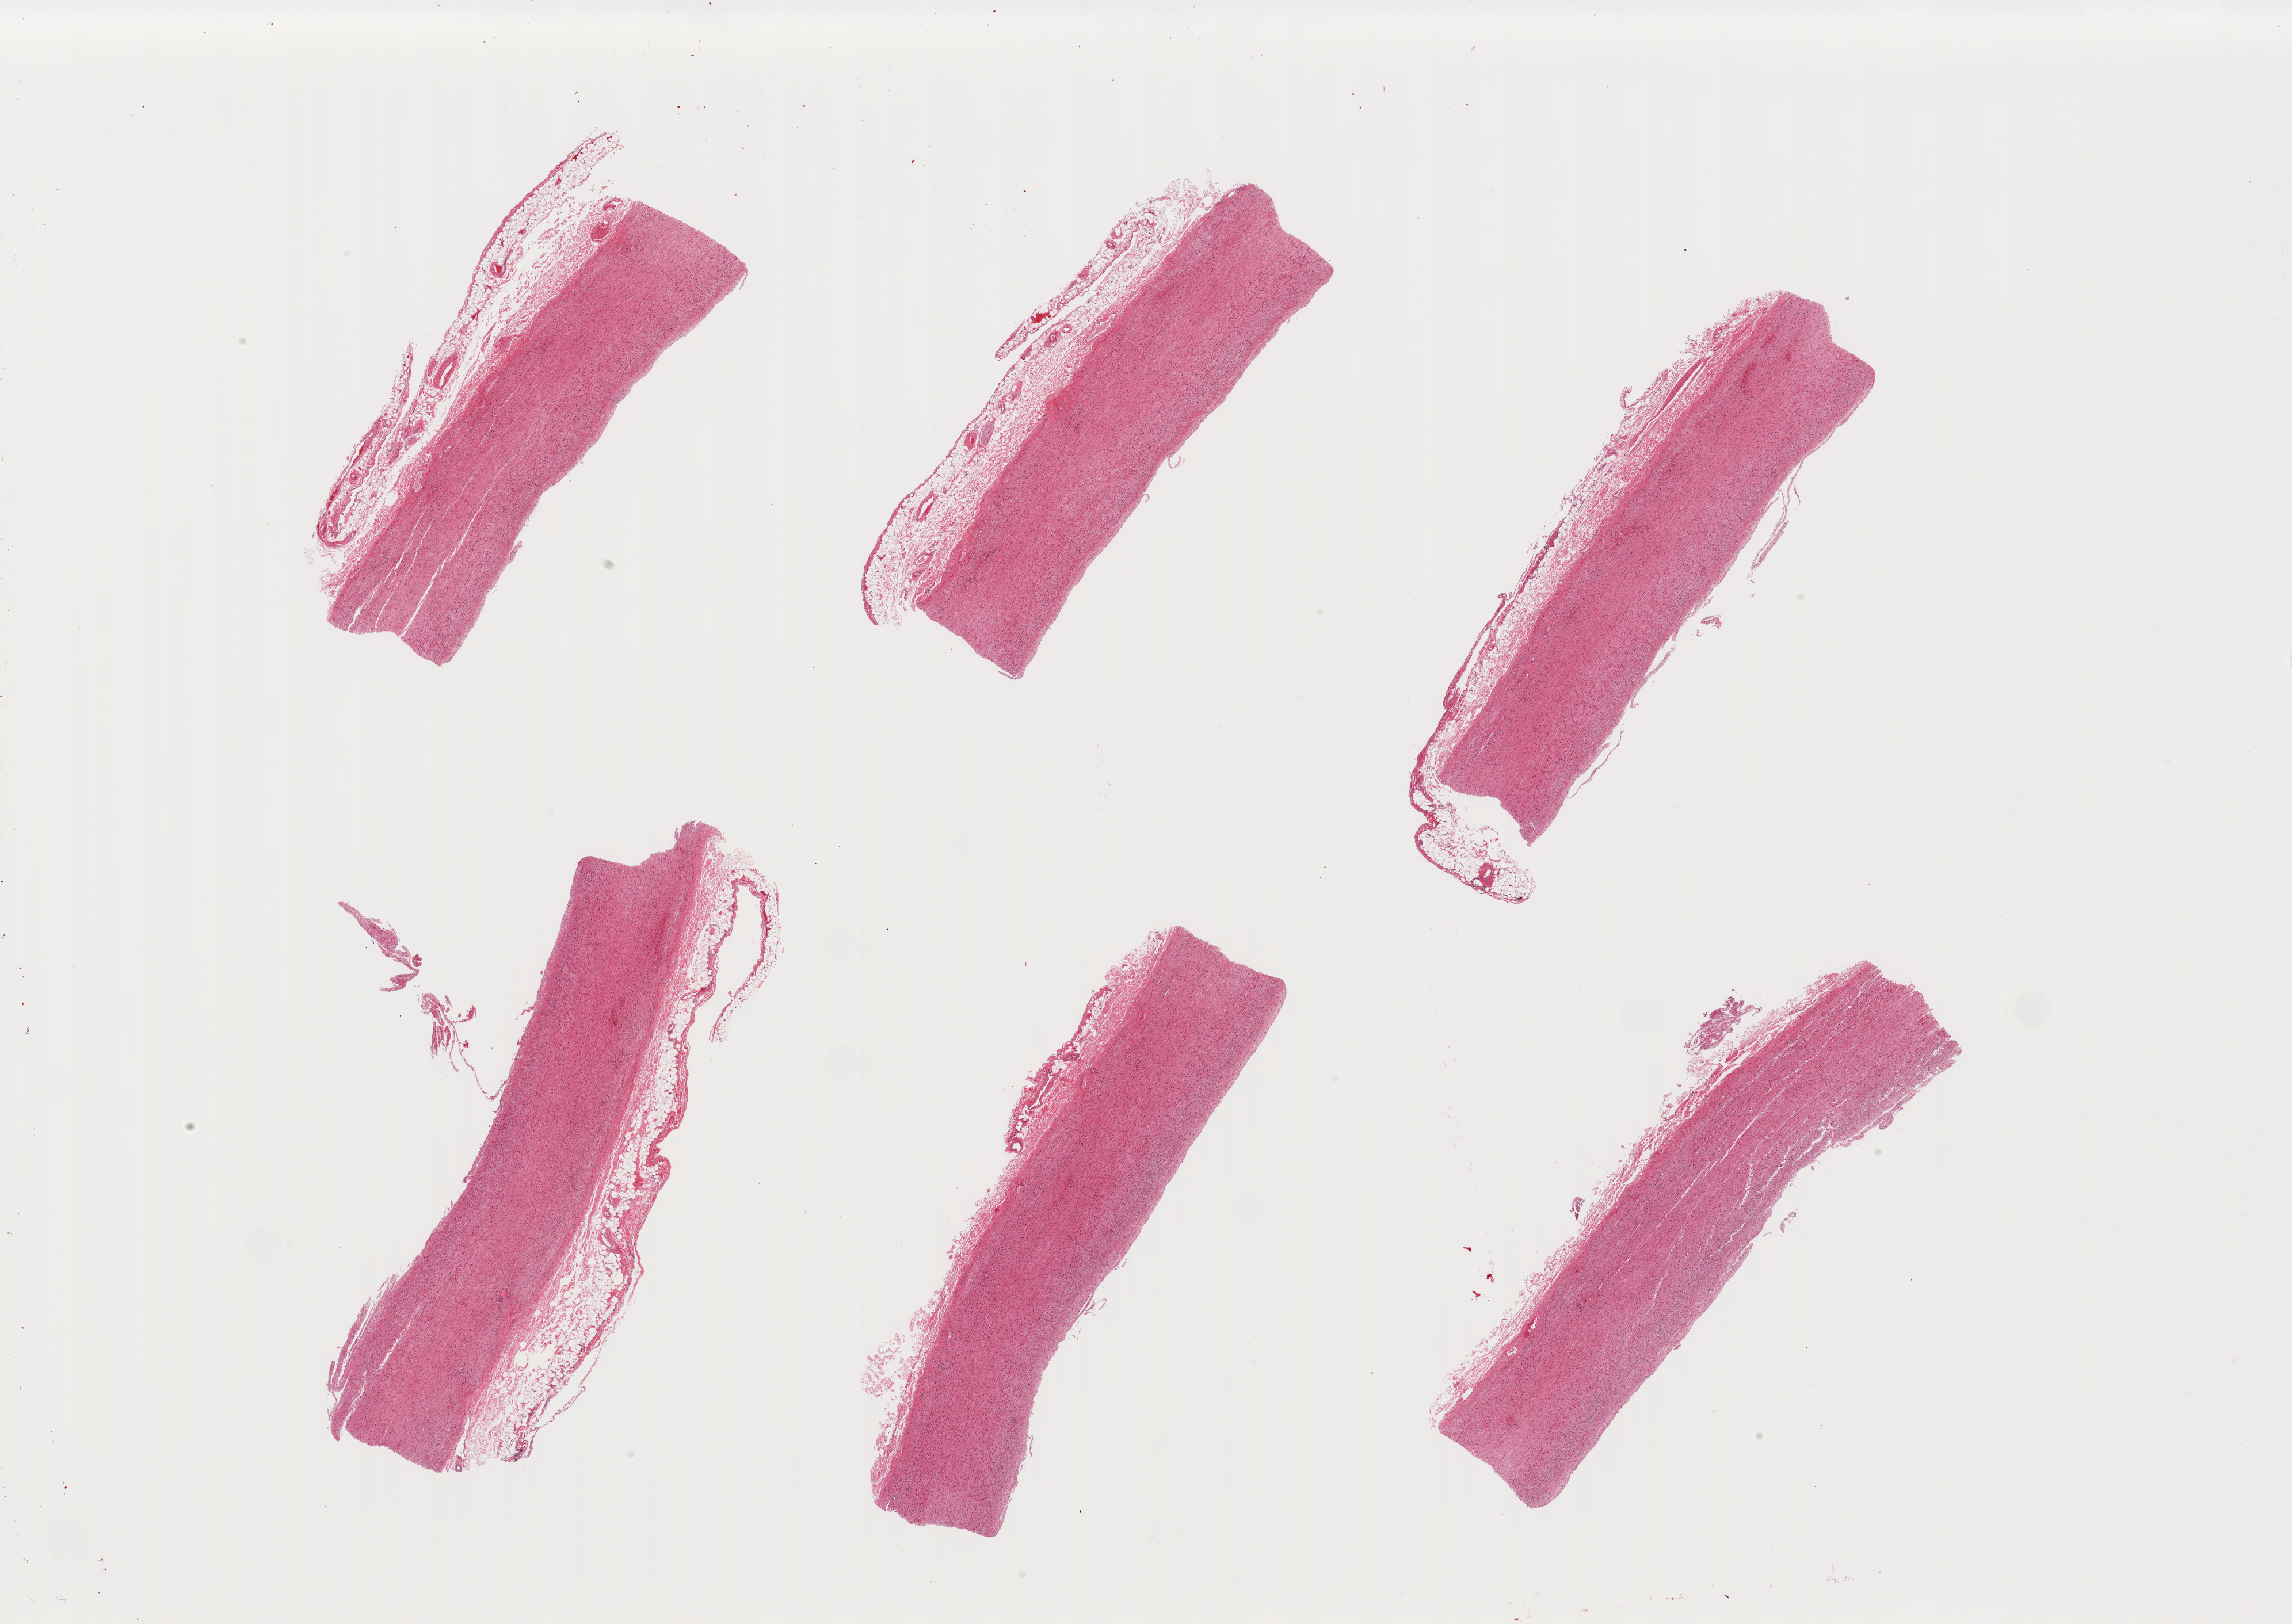
Whole-slide image, H&E stain, brightfield, low-resolution overview of the scanned area, about 31.5 x 22.3 mm (acquisition: 20x scan), PAXgene-fixed, paraffin-embedded tissue, sampled site (target tissue): aorta, tissue donor sample. Donor sex: male.
Reviewer comment on this tissue sample: 6 pieces; over 1mm attached fat.